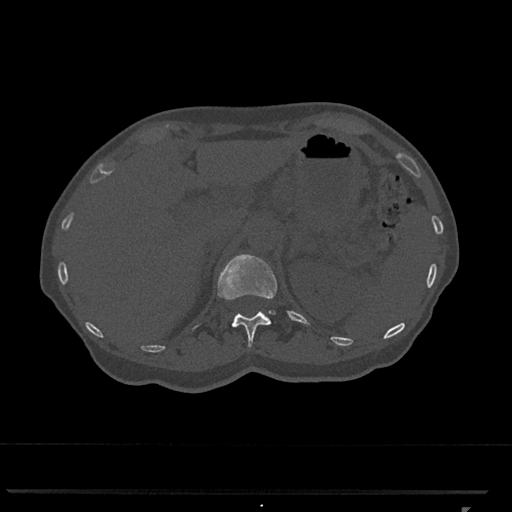
CT including the spine, one axial slice. Position 451 of 793 along the scan axis. Bone window (W 1800 / L 400 HU). 0.5 mm slice thickness. 512 × 512 image matrix, field of view 380 × 380 mm. Patient: female, 62 years. From the clinical record (not read from this slice): primary cancer: renal.
Outlined on this slice (semi-automatic segmentation, software-assisted and operator-edited):
- T12 vertebra: bounding box <217,254,278,347> (left, top, right, bottom; pixels)